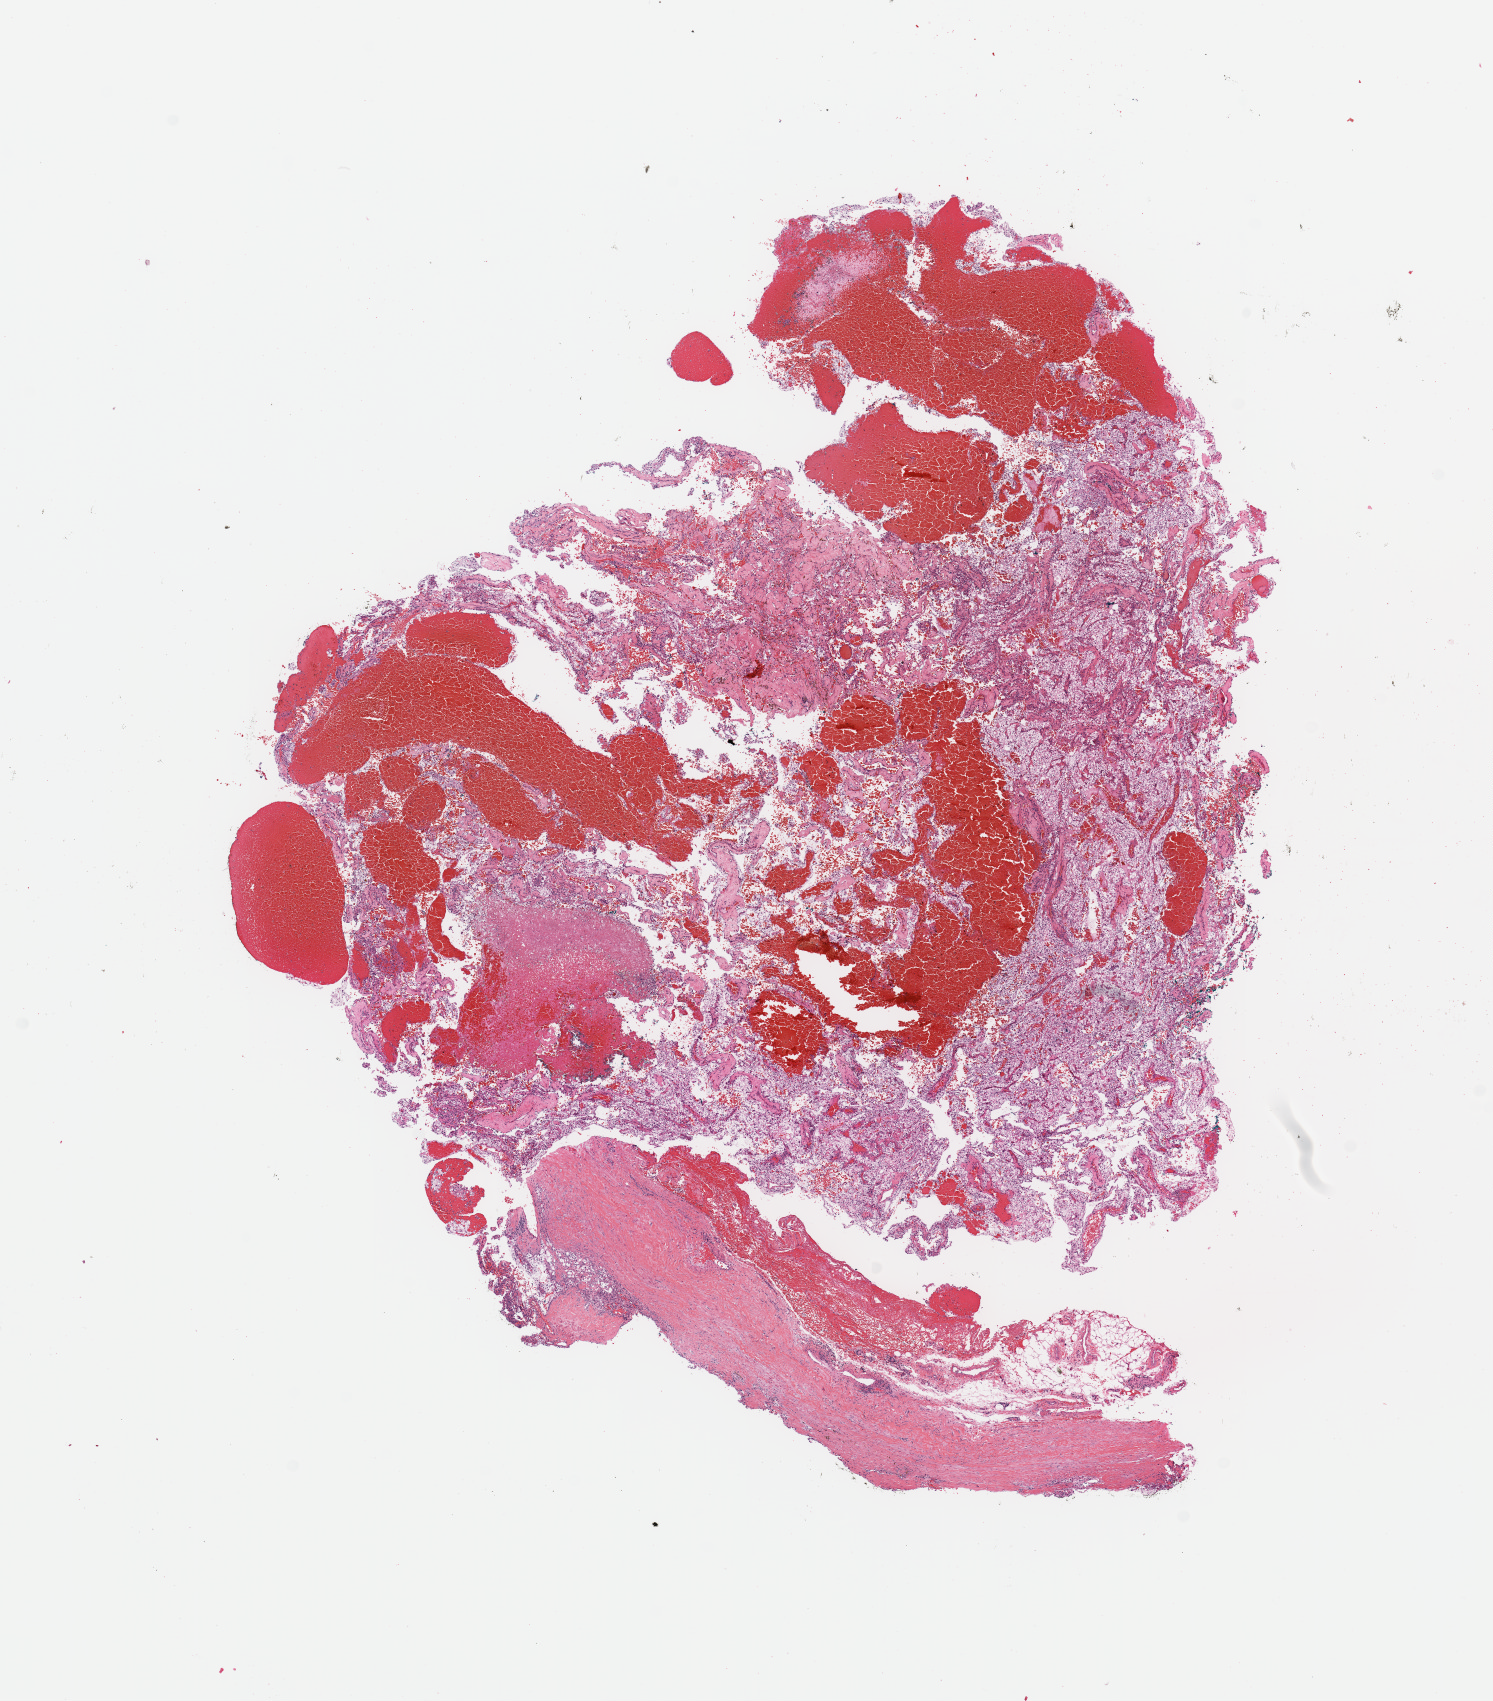
Hematoxylin and eosin (H&E) stained whole-slide image — whole scanned area (about 11.8 x 13.5 mm) shown as a low-resolution overview, kidney, tumour tissue. Male, 63 y/o.
Diagnosis: Renal cell carcinoma, NOS.